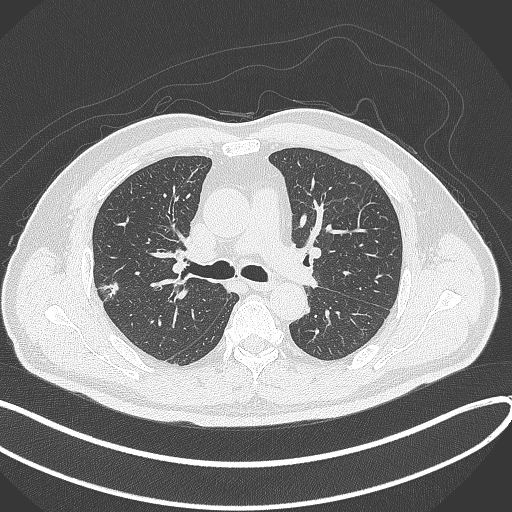
Chest CT, one axial slice; slice 214 of 372 in the series (ordered by position); reconstruction kernel B70f; 120 kVp; lung window (W 1500 / L -600 HU); 1 mm slice thickness; 512 × 512 image matrix, field of view 400 × 400 mm. Male patient, age 60 years. From the clinical record (not read from this slice): clinical TNM (as recorded): T1c N0 M0.
Structures marked on this image (bounding box drawn by a radiologist):
- lung tumour (recorded histology: adenocarcinoma): bounding box <94,278,125,304> (left, top, right, bottom; pixels)